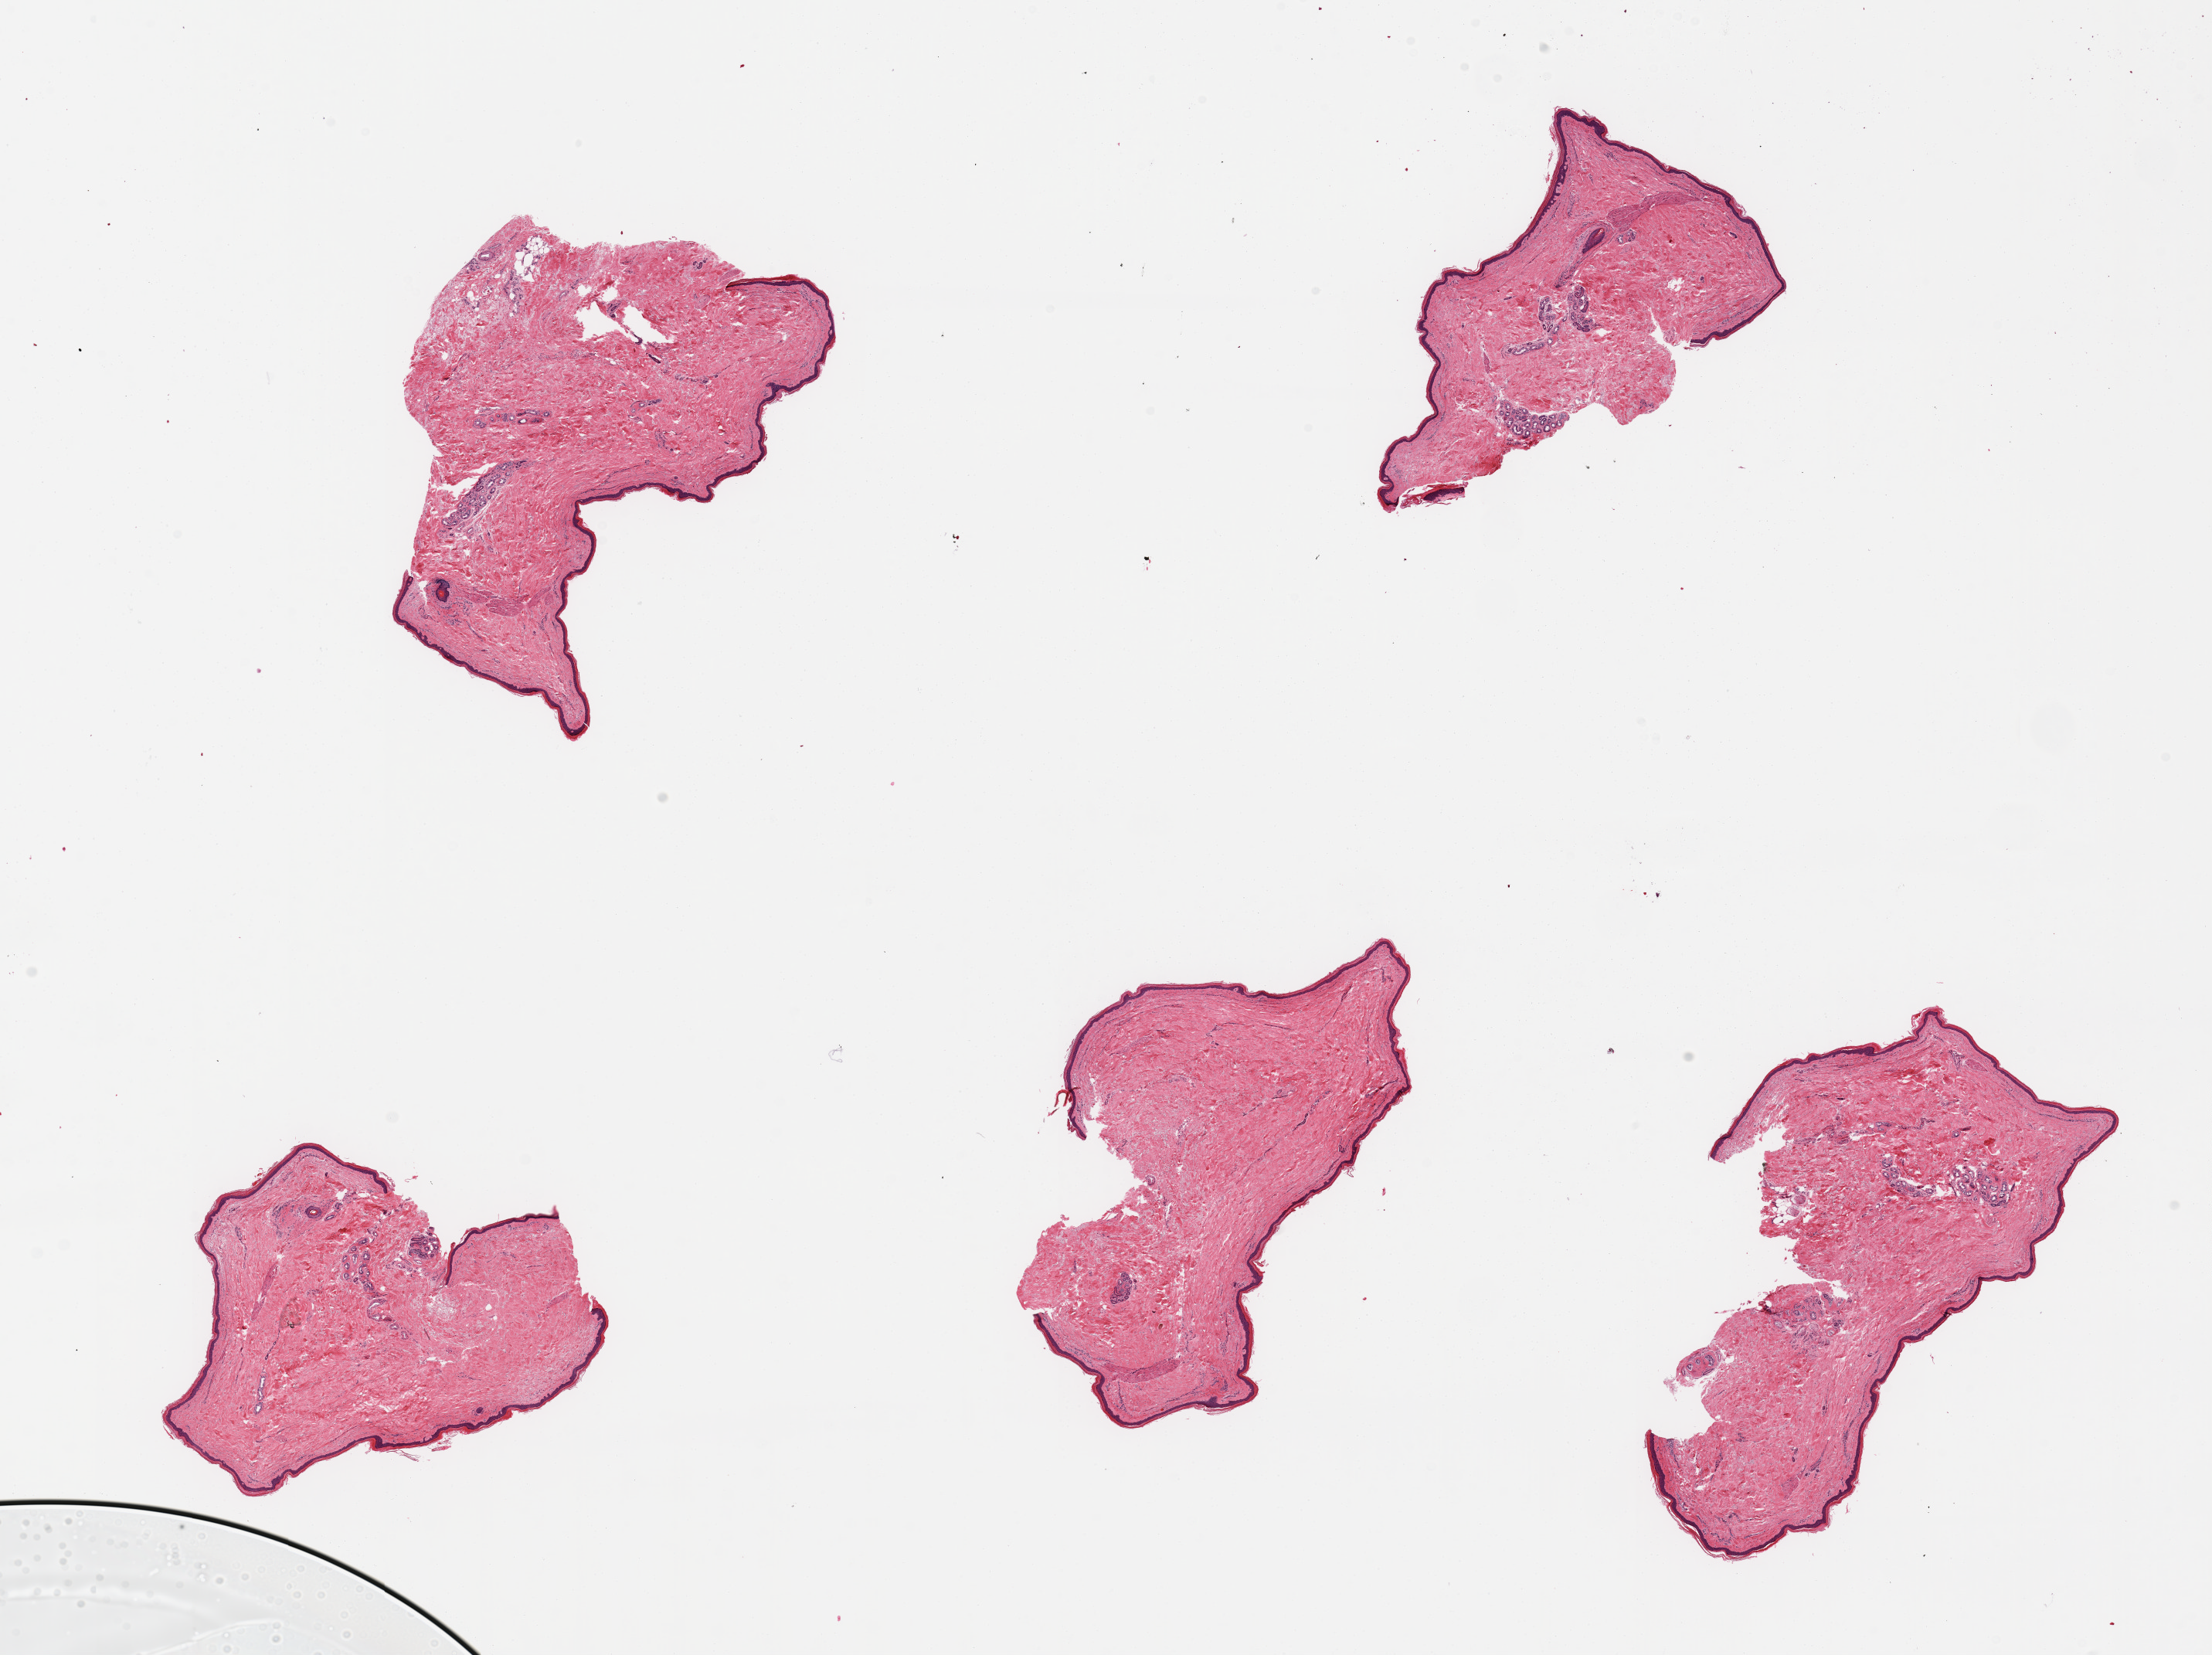
Whole-slide image, haematoxylin and eosin stain, low-resolution overview of the scanned area, about 22.6 x 16.9 mm (from a 20x scan). PAXgene-fixed paraffin-embedded (PFPE) section. Section of skin of lower leg (target tissue). Tissue donor sample. Donor: male.
Review note (as recorded): 5 pieces; well trimmed epidermis measures 35 microns.